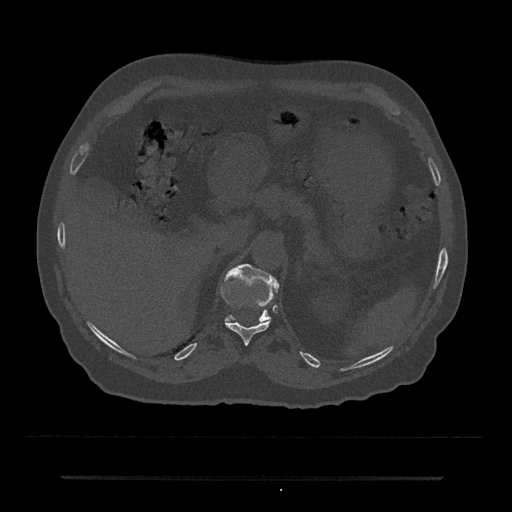
CT including the spine, one axial slice. Position 165 of 797 along the scan axis. Reconstruction kernel Br40s/3. 120 kVp. Bone window (W 1800 / L 400 HU). 512 × 512 image matrix. Male patient, age 69 years. From the clinical record (not read from this slice): primary cancer: prostate.
Annotated regions visible in this slice (semi-automatic segmentation, software-assisted and operator-edited):
- T11 vertebra: bounding box (x1, y1, x2, y2) in pixels: (225, 304, 270, 345)
- T12 vertebra: (225, 264, 279, 322)